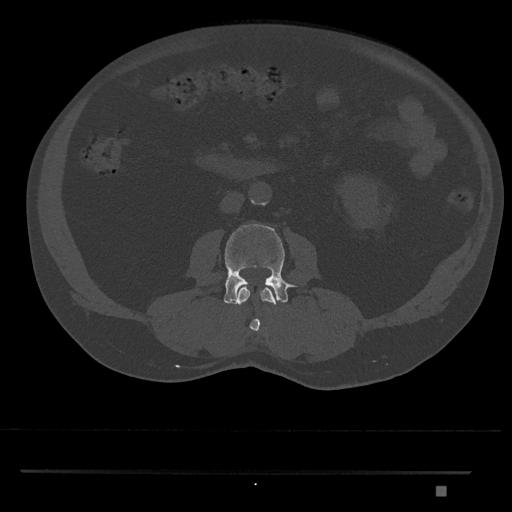
CT including the spine, one axial slice. Reconstruction kernel Br40s/3. 120 kVp. Bone window (W 1800 / L 400 HU). 0.5 mm slice thickness. 512 × 512 image matrix, field of view 429 × 429 mm. Male patient, age 65 years. Case-level facts recorded for this patient, not image findings: primary cancer: prostate.
Outlined on this slice (semi-automatic segmentation, software-assisted and operator-edited):
- L2 vertebra: bounding box <237,287,276,333> (left, top, right, bottom; pixels)
- L3 vertebra: <223,224,296,305>